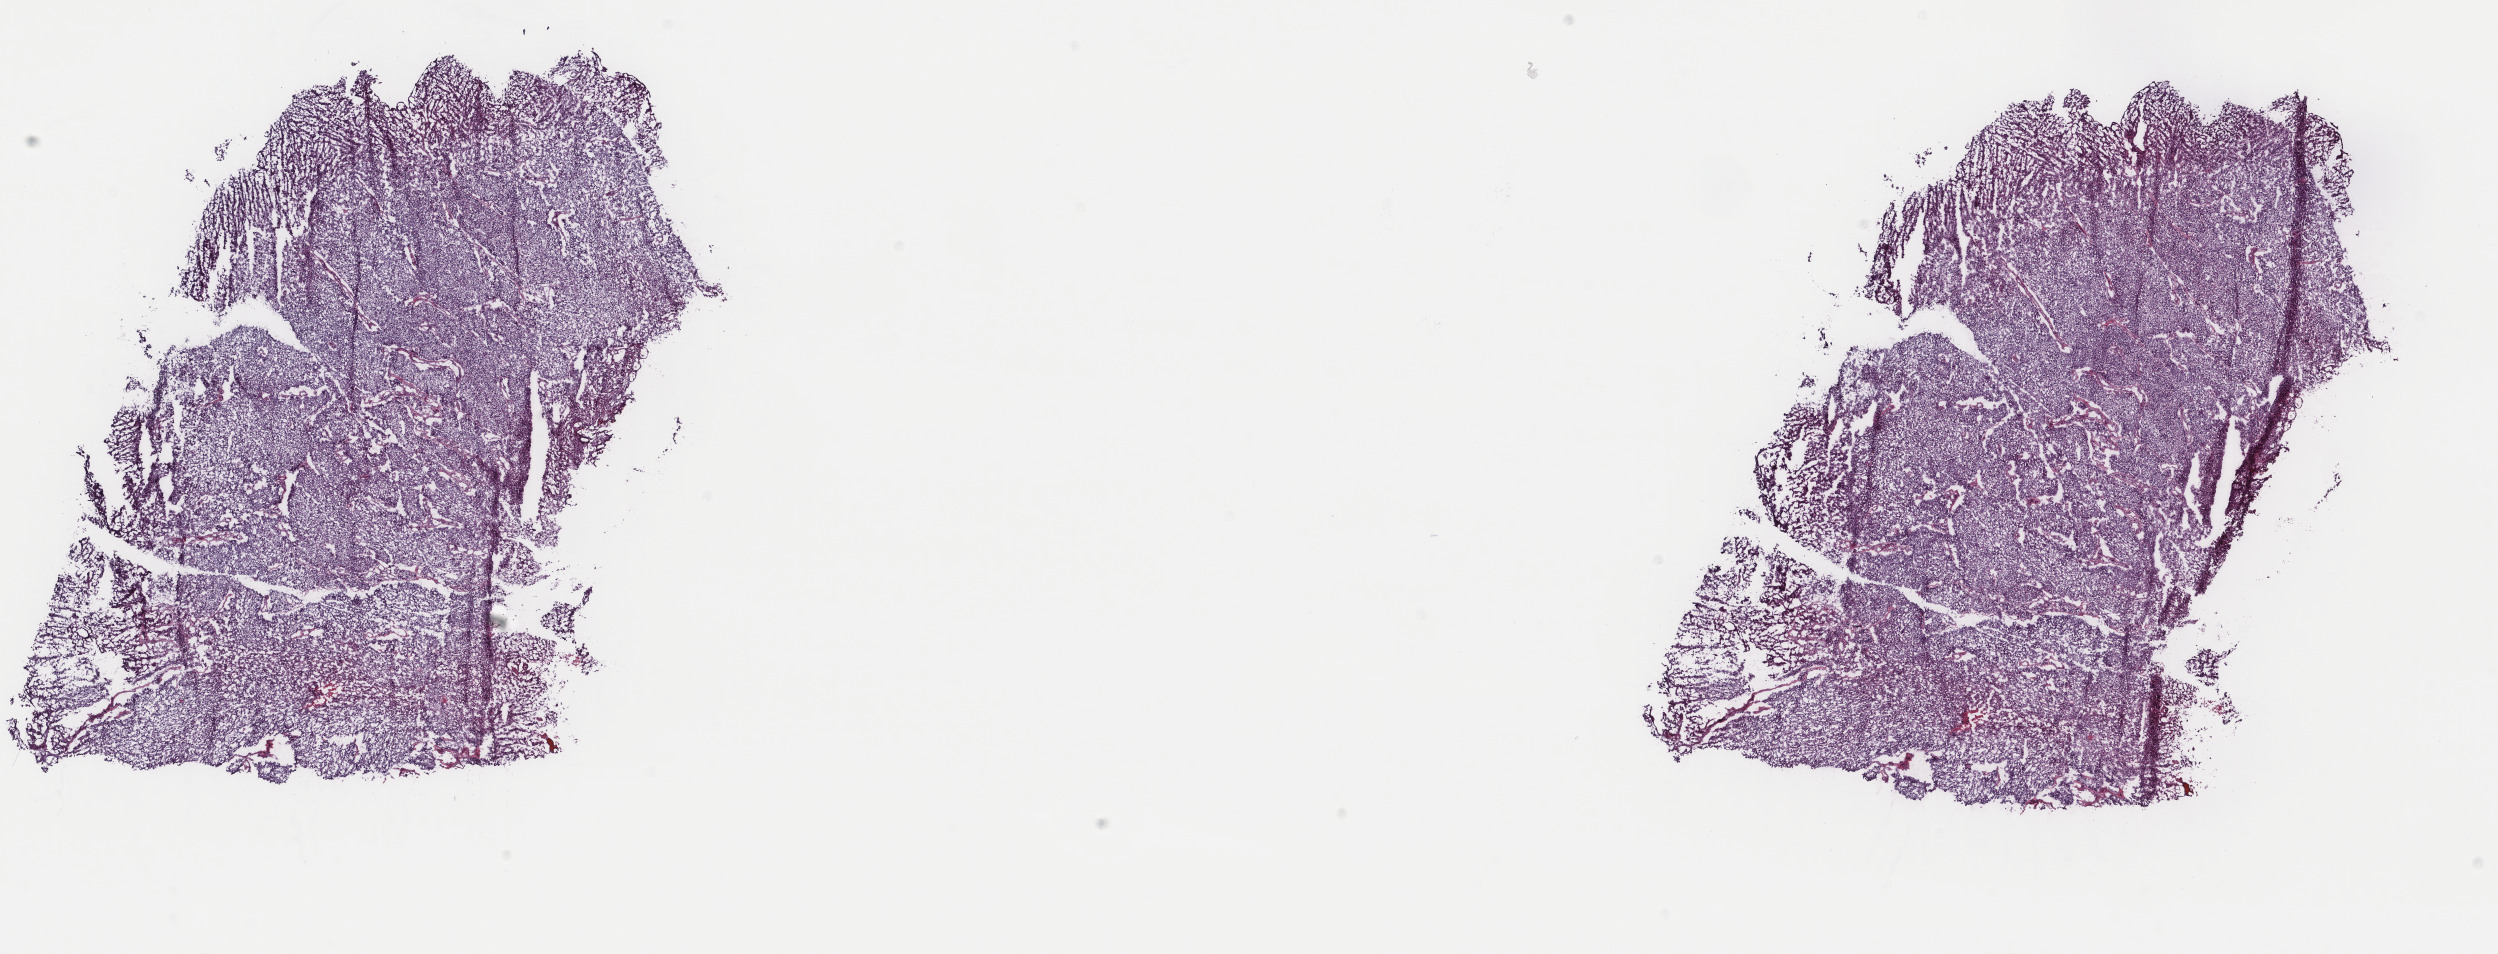
Digitized H&E tissue section (whole slide) — a low-resolution overview of the entire scanned area, about 19.8 x 7.6 mm (from a 40x scan); frozen section; sample: primary tumour, bladder. Male patient; age at initial diagnosis 65 years. Histologic grade: high grade. Slide review estimates, as recorded: tumour cells 85%, tumour nuclei 85%, normal cells 0%, stromal cells 14%, necrosis 1%. Infiltration values recorded for this section: lymphocyte infiltration 4%, monocyte infiltration 1%, neutrophil infiltration 2%.
AJCC pathologic stage: IV. TNM: N3 M1. Diagnosis: Transitional cell carcinoma.